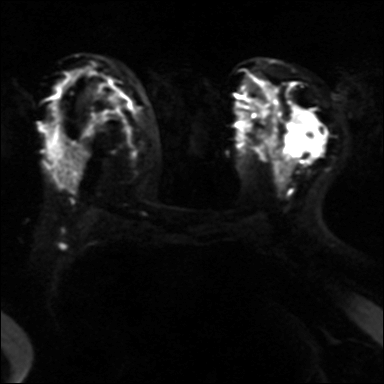
Breast MRI, one axial slice; position 20 of 40 along the scan axis; diffusion-weighted series; image 2 of 4 stored at this slice position (different b-values; order by instance number); 3 T; 384 × 384 image matrix. Female patient.
Annotated regions visible in this slice (expert manual segmentation):
- tumour on diffusion-weighted imaging: bounding box [x1, y1, x2, y2] px = [291, 112, 320, 154]